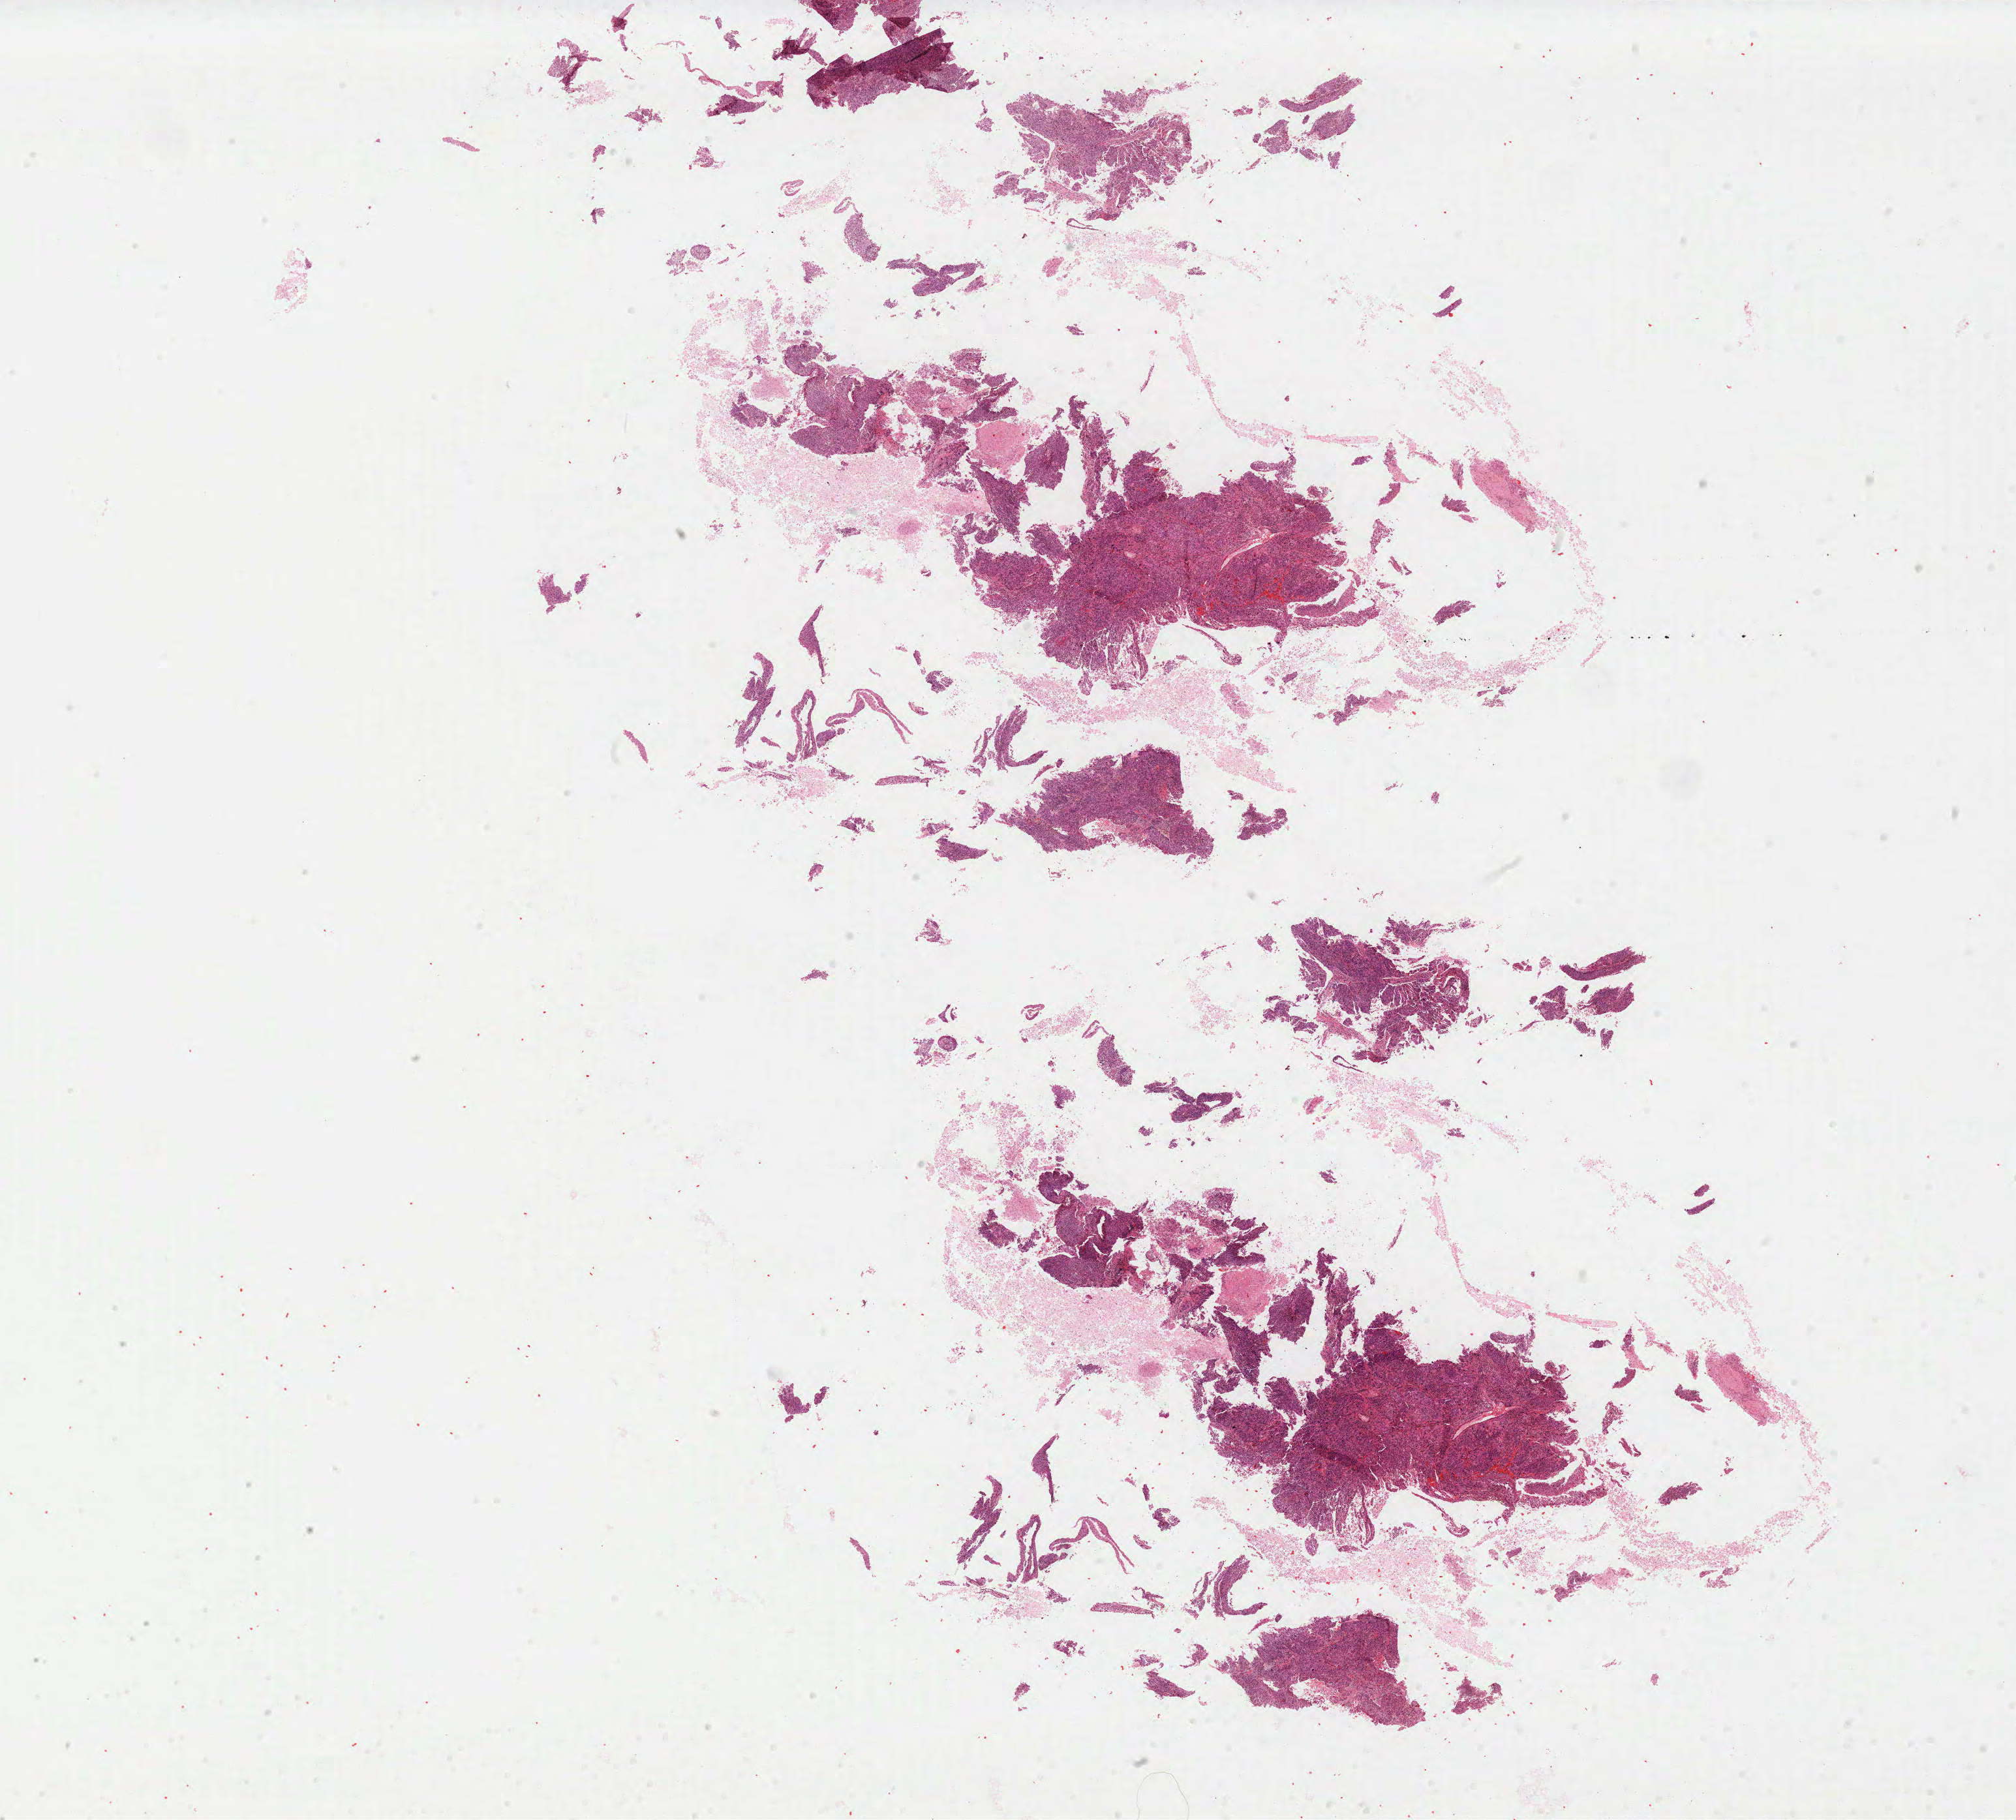
Digitized H&E tissue section (whole slide) — low-resolution overview of the scanned area, about 24.7 x 22.3 mm (slide scanned at 40x). FFPE section. Sample: primary tumour, cervix. Patient: female, age at initial diagnosis 79 years. Histologic grade: G3 (poorly differentiated).
FIGO stage: IIIB. Histologic diagnosis: Squamous cell carcinoma, NOS (cervix uteri).